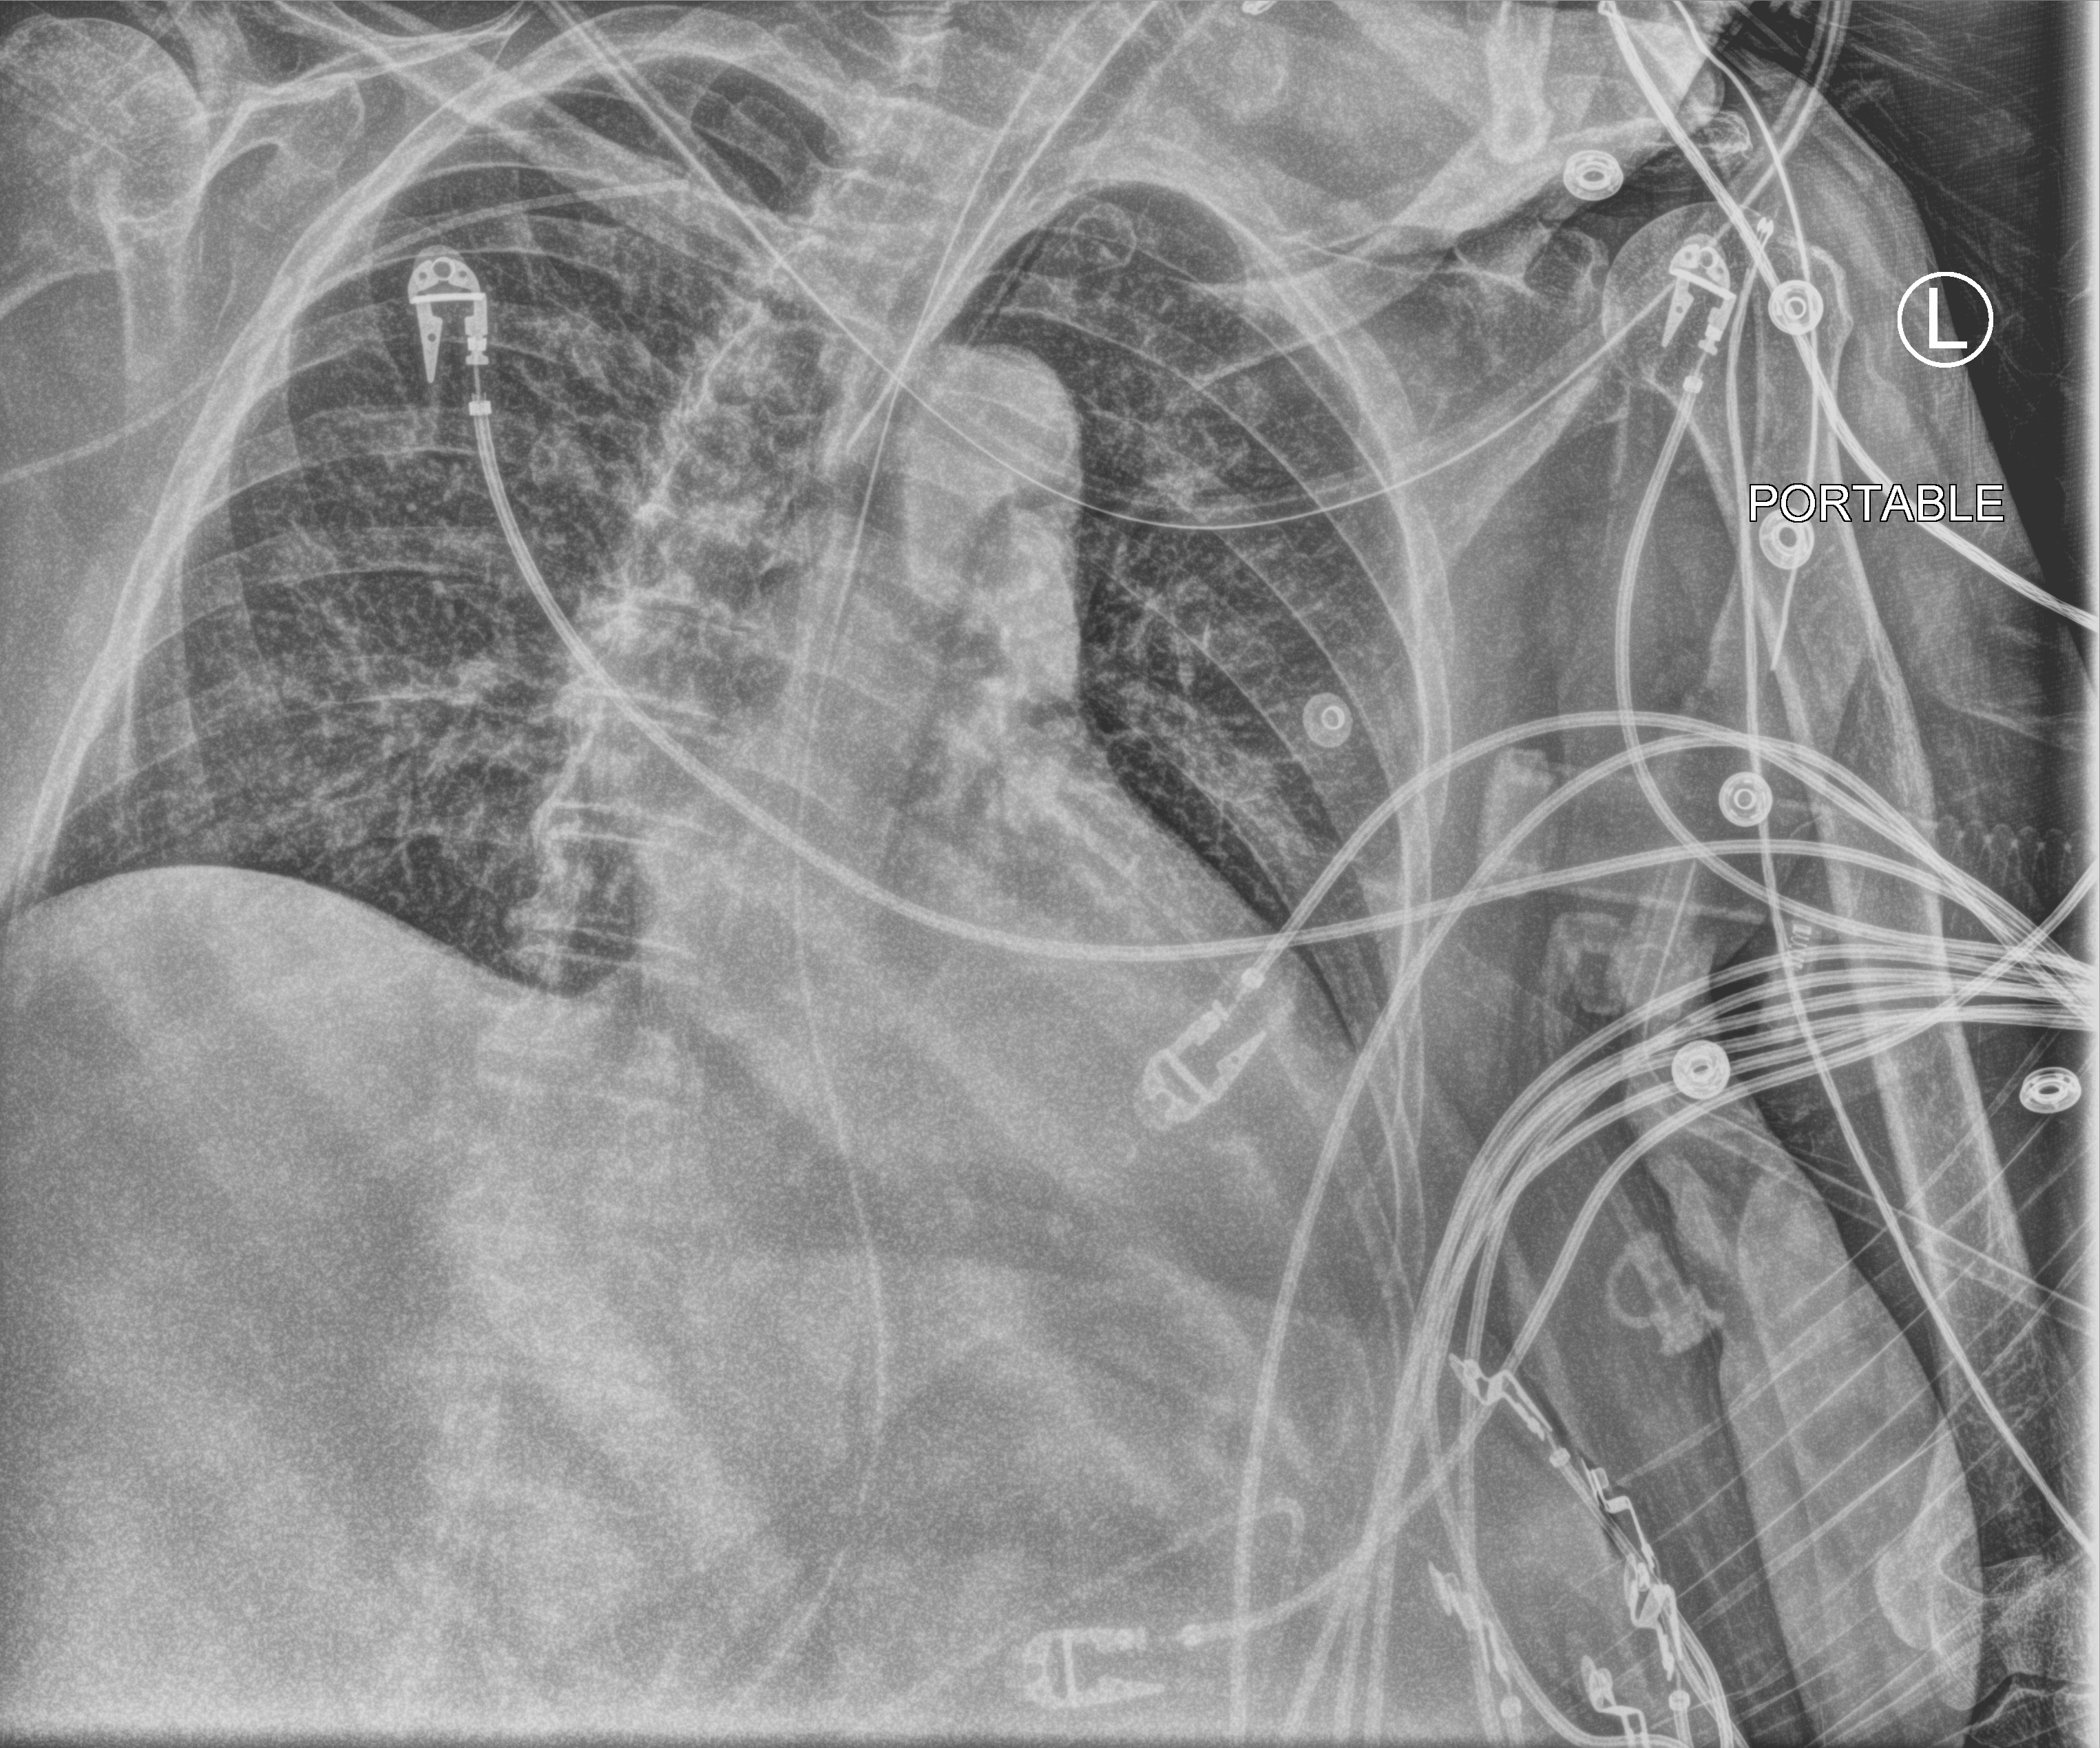
Bedside chest radiograph (computed radiography); anteroposterior (AP) projection. Female patient hospitalised with COVID-19, age 75–90 years.
From the hospital-stay record, not from the radiograph (when in the stay this image was taken is not recorded): hypertension (admission record): yes; admitted to intensive care during this hospital stay: yes.